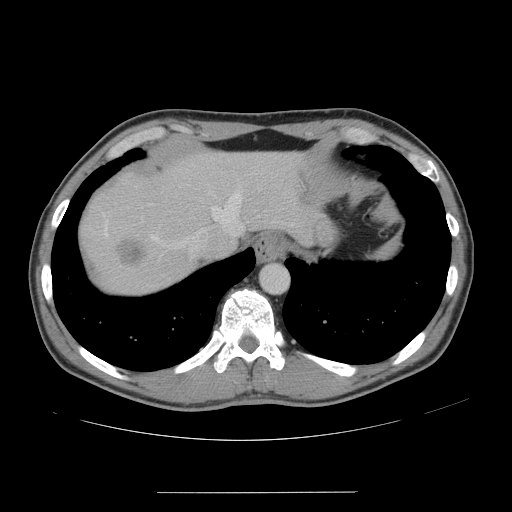
Contrast-enhanced abdominal CT, one axial slice. Position 131 of 178 along the scan axis. 120 kVp. Intravenous contrast given. Soft-tissue window (W 400 / L 40 HU). 2.5 mm slice thickness. 512 × 512 image matrix. Male patient, age 53 years. Case-level facts recorded for this patient, not image findings: diagnosis: colorectal cancer liver metastases, imaged before liver resection; multiple liver metastases: yes; largest metastasis: 2.4 cm; chemotherapy before resection: yes.
Outlined on this slice (outlined manually by an expert reader):
- hepatic veins: bounding box (x1, y1, x2, y2) in pixels: (104, 186, 244, 252)
- liver: (81, 153, 307, 294)
- planned liver remnant (the part of the liver to remain after resection): (173, 153, 308, 245)
- liver metastasis: (116, 239, 147, 268)